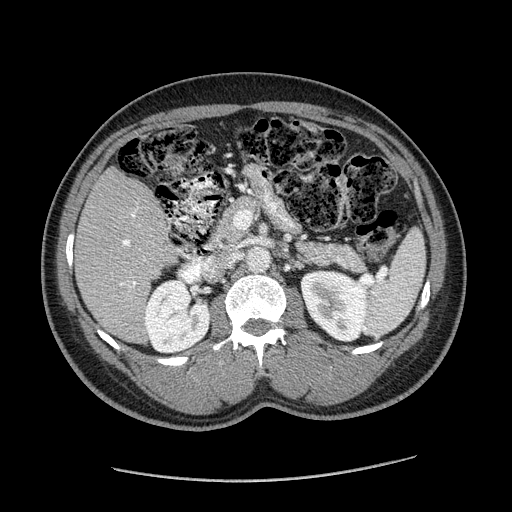
Contrast-enhanced abdominal CT (liver protocol), one axial slice. Slice 79 of 182 in the series (ordered by position). Reconstruction kernel STANDARD. 120 kVp. Soft-tissue window (W 400 / L 40 HU). 512 × 512 image matrix. Case-level facts recorded for this patient, not image findings: diagnosis: hepatocellular carcinoma (patient treated with transarterial chemoembolisation; whether this scan precedes or follows treatment is not stated here); TNM stage (as recorded): Stage-I; Child-Pugh class: A; tumour differentiation: well differentiated; tumour nodularity: uninodular.
Annotated regions visible in this slice (semi-automatic segmentation, software-assisted and operator-edited):
- liver parenchyma outside the tumour (the mass and vessels are separate outlines, so this box may not span the whole liver): bounding box (x1, y1, x2, y2) in pixels: (74, 167, 172, 342)
- liver vessels: (120, 214, 137, 287)